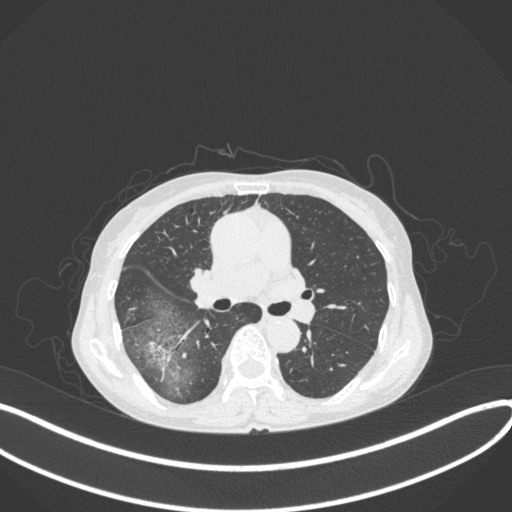
Chest CT, one axial slice. Slice 231 of 379 in the series (ordered by position). Reconstruction kernel B31f. Lung window (W 1500 / L -600 HU). 1 mm slice thickness. 512 × 512 image matrix, field of view 400 × 400 mm. Patient: female, 69 years. From the clinical record (not read from this slice): clinical TNM (as recorded): T1b N0 M0; histopathological grade: G2-3.
Outlined on this slice (rectangle marked by the reading radiologist):
- lung tumour (recorded histology: adenocarcinoma): bounding box (x1, y1, x2, y2) in pixels: (145, 334, 187, 384)